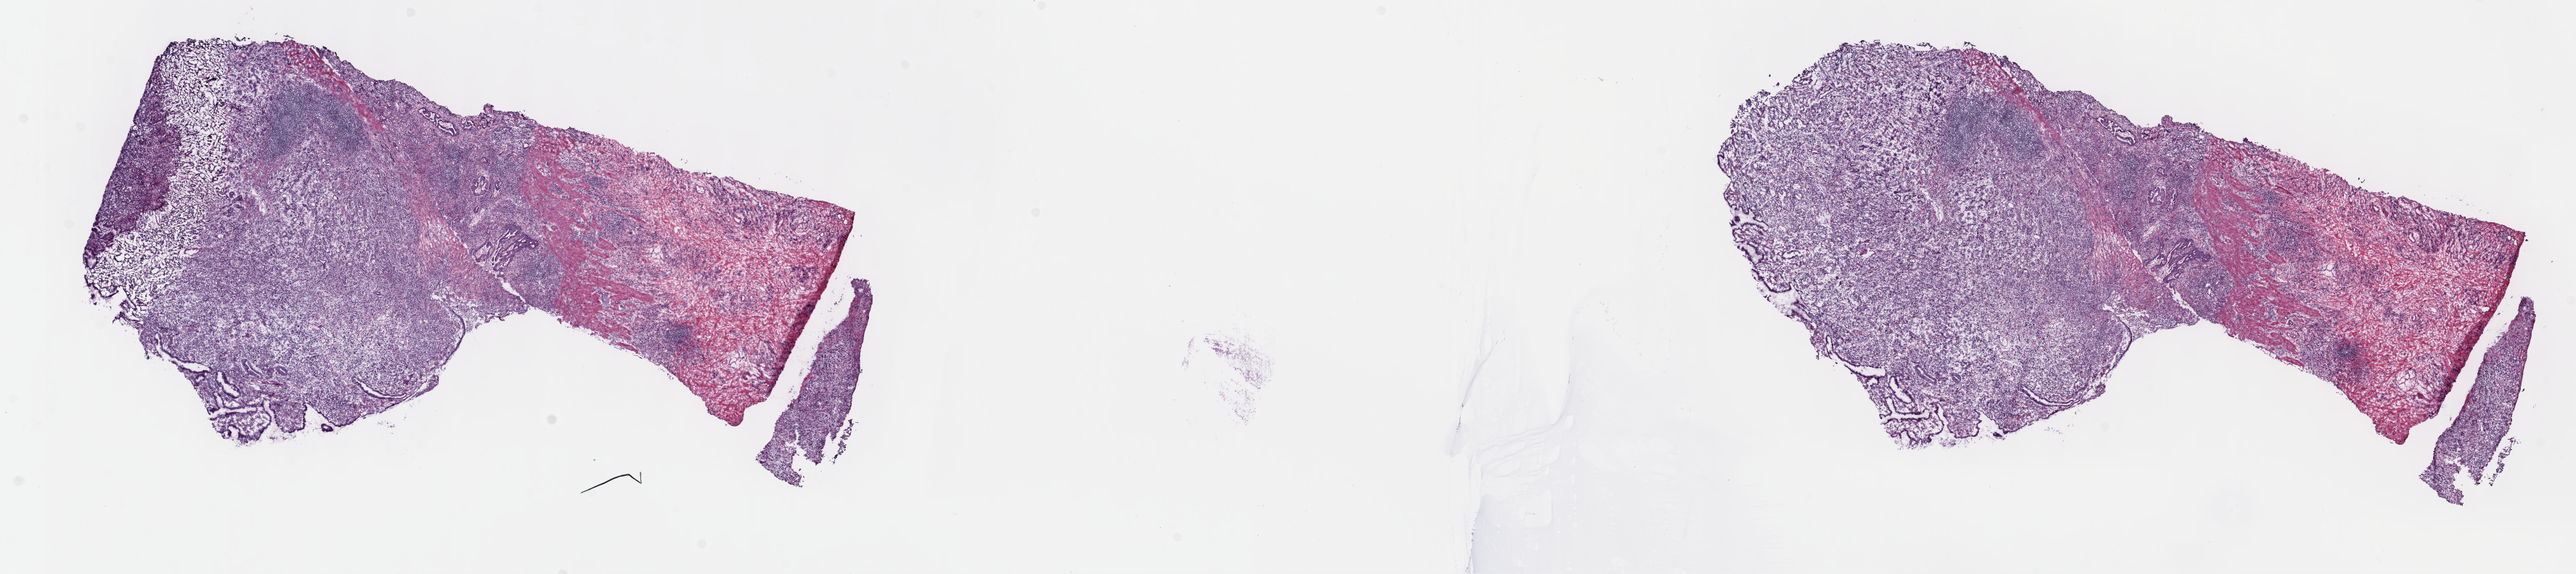
H&E-stained whole-slide image — whole scanned area (about 28.7 x 6.4 mm) shown as a low-resolution overview; frozen section from the top of the tissue portion; stomach, primary tumour sample. Patient: male, age at initial diagnosis 69 years. Histologic grade: G2 (moderately differentiated). Pathologist review of this section (percent, as recorded): tumour cells 70%, tumour nuclei 80%, normal cells 10%, stromal cells 20%, necrosis 0%. Infiltration values recorded for this section: lymphocyte infiltration 0%, monocyte infiltration 0%, neutrophil infiltration 0%.
Pathologic diagnosis: Adenocarcinoma, NOS (body of stomach). AJCC pathologic stage: IIIC (7th edition).